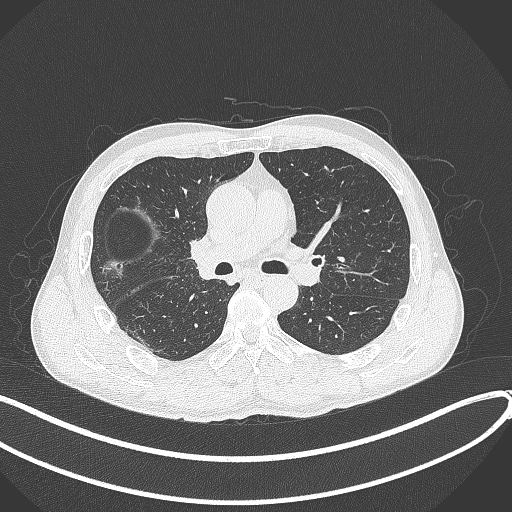
Chest CT, one axial slice; position 228 of 409 along the scan axis; lung window (W 1500 / L -600 HU); 1 mm slice thickness; 512 × 512 image matrix. Patient: male, 53 years. Case-level facts recorded for this patient, not image findings: clinical TNM (as recorded): T1b N0 M0.
Outlined on this slice (bounding box drawn by a radiologist):
- lung tumour (recorded histology: squamous cell carcinoma): box from (x=186, y=234) to (x=226, y=287) px